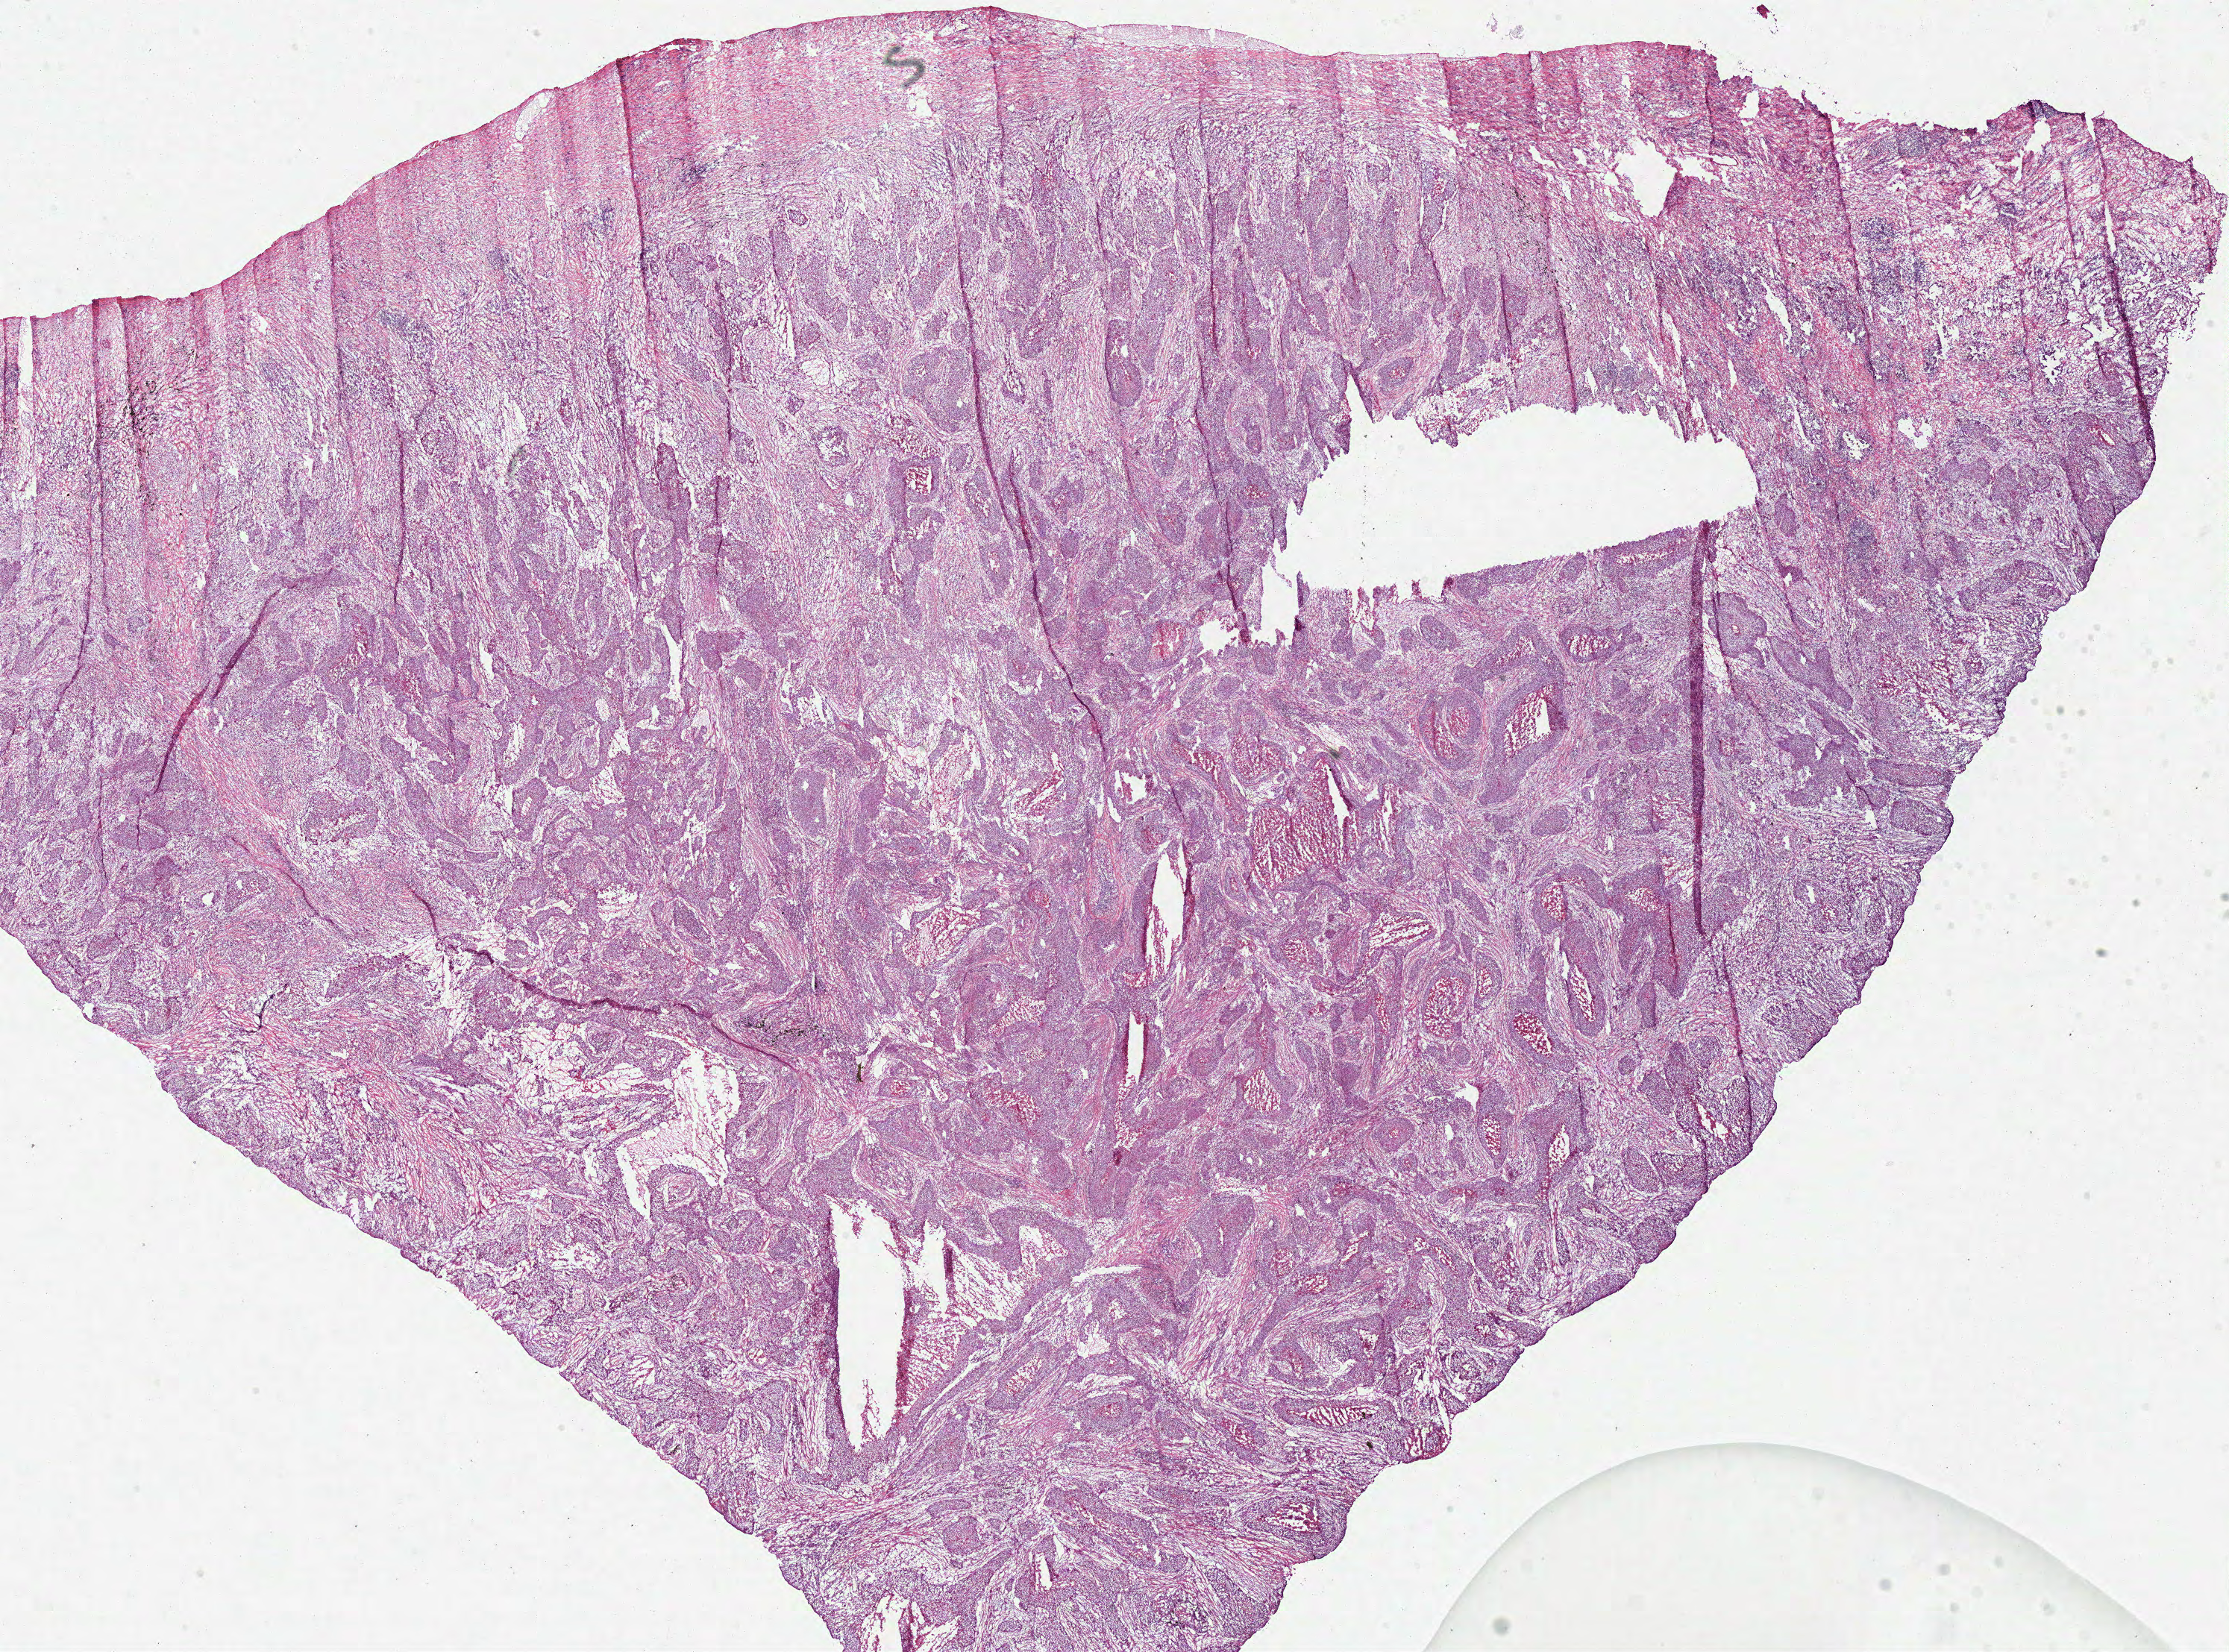
Whole-slide histology image, H&E, a low-resolution overview of the entire scanned area, about 23.5 x 17.4 mm, frozen section, primary tumour sample from the lung. Male, age 57 years at initial diagnosis. Slide review estimates, as recorded: tumour cells 70%, tumour nuclei 75%, normal cells 0%, stromal cells 10%, necrosis 20%.
Histologic diagnosis: Squamous cell carcinoma, NOS (upper lobe, lung). AJCC pathologic stage: IIIA. TNM: T3 N1 M0.